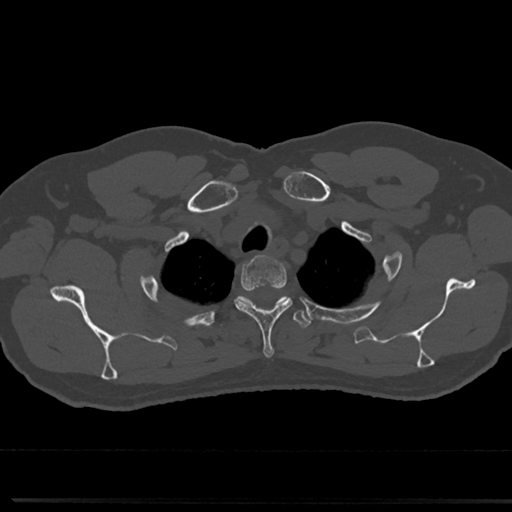
CT including the spine, one axial slice; slice 623 of 817 in the series (ordered by position); 120 kVp; bone window (W 1800 / L 400 HU); 0.5 mm slice thickness; 512 × 512 image matrix, field of view 355 × 355 mm. Male patient, age 61 years. Case-level facts recorded for this patient, not image findings: primary cancer: prostate.
Structures marked on this image (semi-automatically segmented with operator editing):
- T2 vertebra: box from (x=234, y=259) to (x=289, y=355) px
- T3 vertebra: (x=216, y=294)–(x=313, y=332)